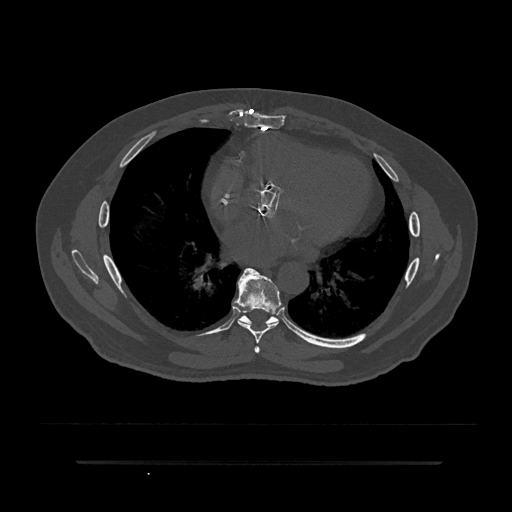
CT including the spine, one axial slice. Slice 460 of 797 in the series (ordered by position). 120 kVp. Bone window (W 1800 / L 400 HU). 512 × 512 image matrix, field of view 464 × 464 mm. Male patient, age 59 years. From the clinical record (not read from this slice): primary cancer: bile ducts; vertebrae with lytic lesions (as recorded): T10.
Outlined on this slice (semi-automatically segmented with operator editing):
- T6 vertebra: bounding box [x1, y1, x2, y2] px = [254, 346, 260, 353]
- T7 vertebra: [233, 268, 282, 343]
- T8 vertebra: [238, 308, 297, 334]